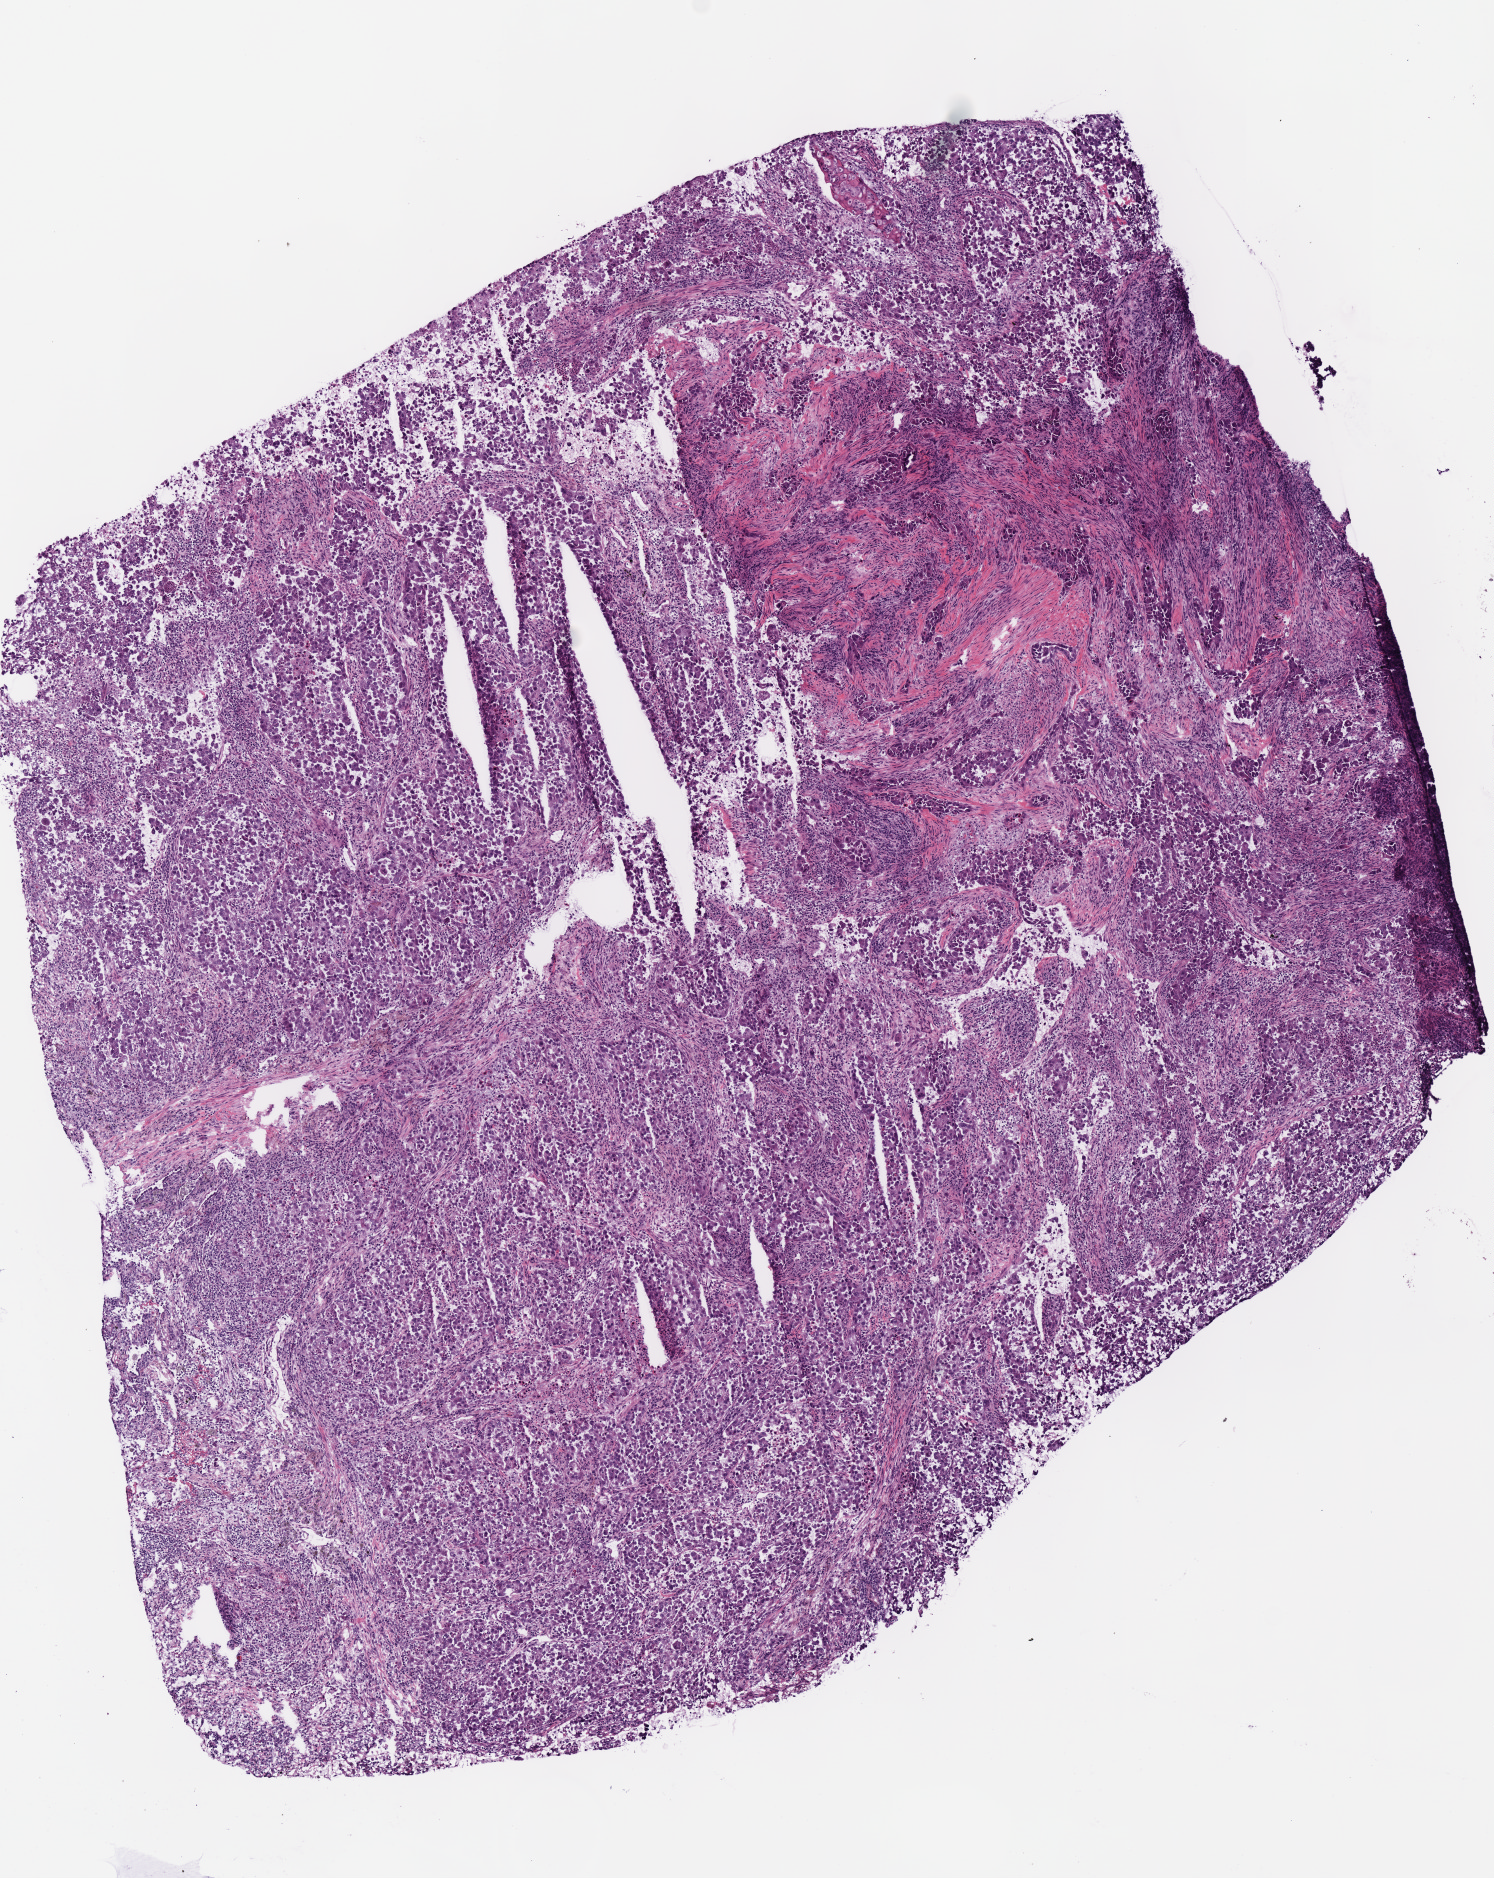
Digitized Hematoxylin and eosin (H&E) stained tissue section (whole slide), low-resolution overview of the scanned area, about 5.9 x 7.4 mm, frozen section from the bottom of the tissue portion, primary tumour sample from the lung. Male, age 61 years at initial diagnosis. Slide review estimates, as recorded: tumour cells 73%, tumour nuclei 50%, normal cells 5%, stromal cells 20%, necrosis 2%.
• diagnosis: Adenocarcinoma, NOS (upper lobe, lung)
• AJCC pathologic stage: IB (7th edition)